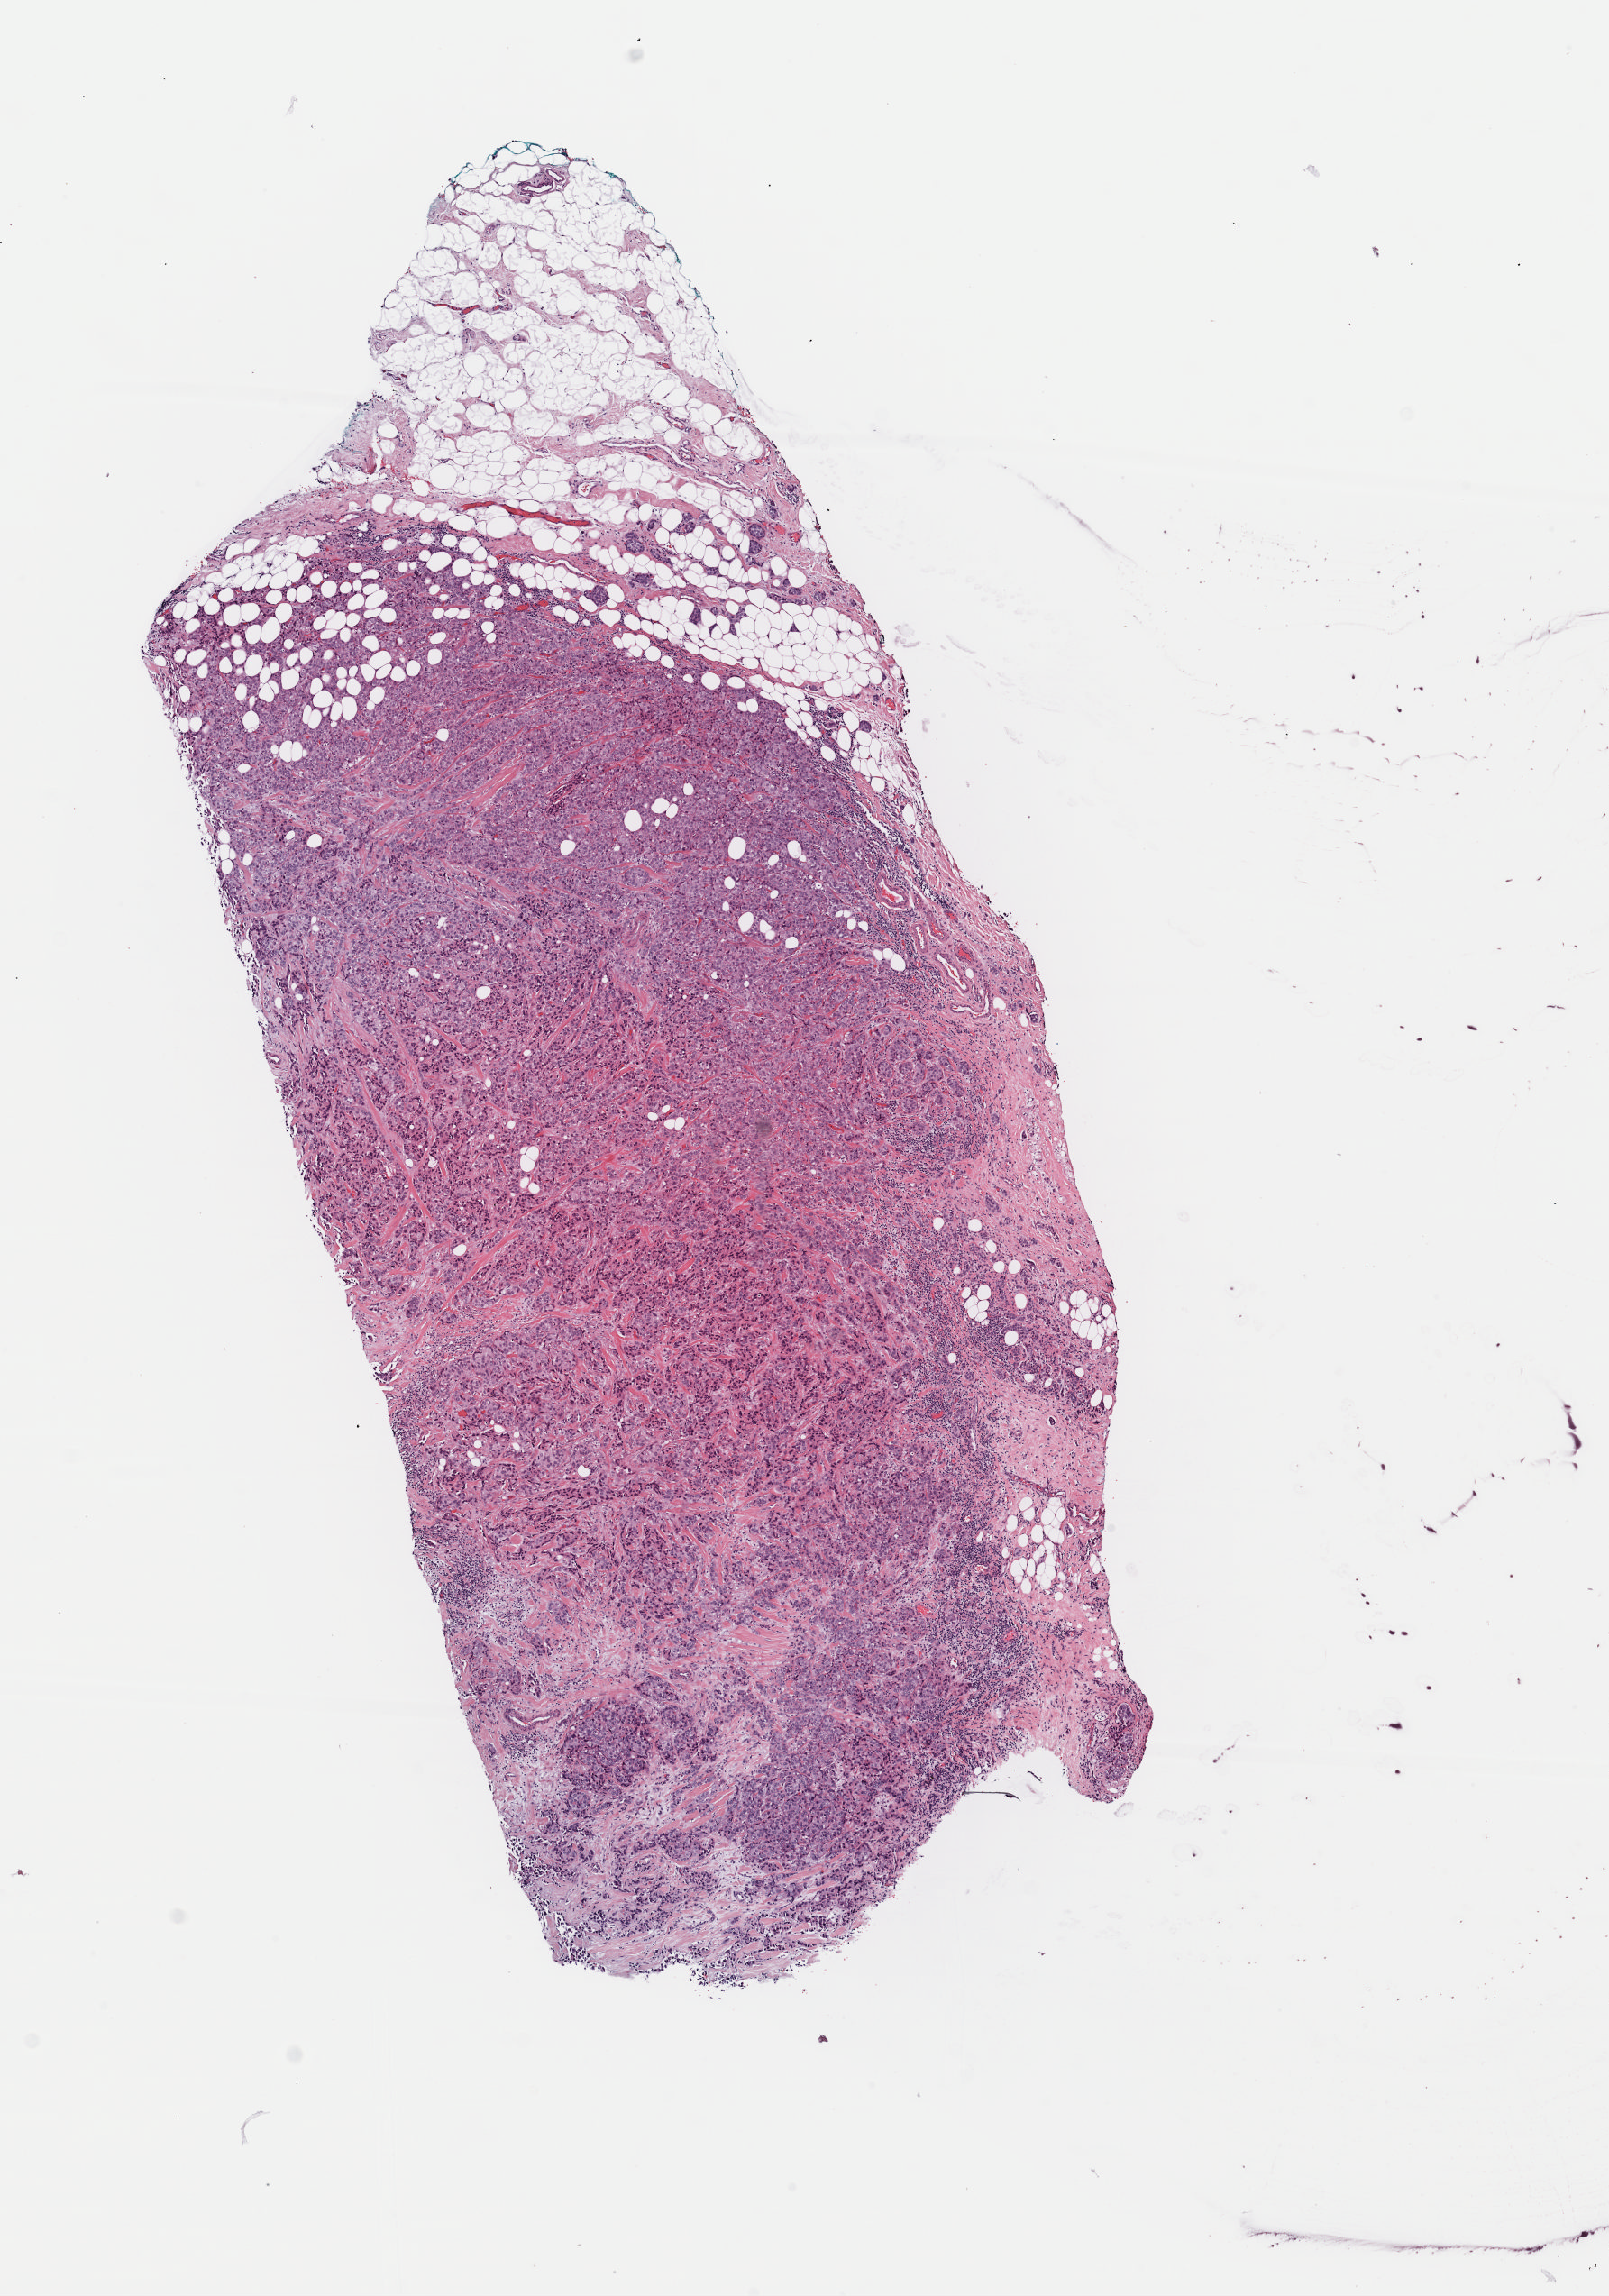
Whole-slide histology image, H&E — whole scanned area (about 7.0 x 10.1 mm, acquisition: 40x scan) shown as a low-resolution overview. Formalin-fixed paraffin-embedded (FFPE) diagnostic section. Breast, primary tumour sample. Female patient; age at initial diagnosis 54 years.
Histologic diagnosis: Infiltrating duct carcinoma, NOS. AJCC pathologic stage: IIA (7th edition). Lymph nodes positive (case pathology): 0 of 2 examined.